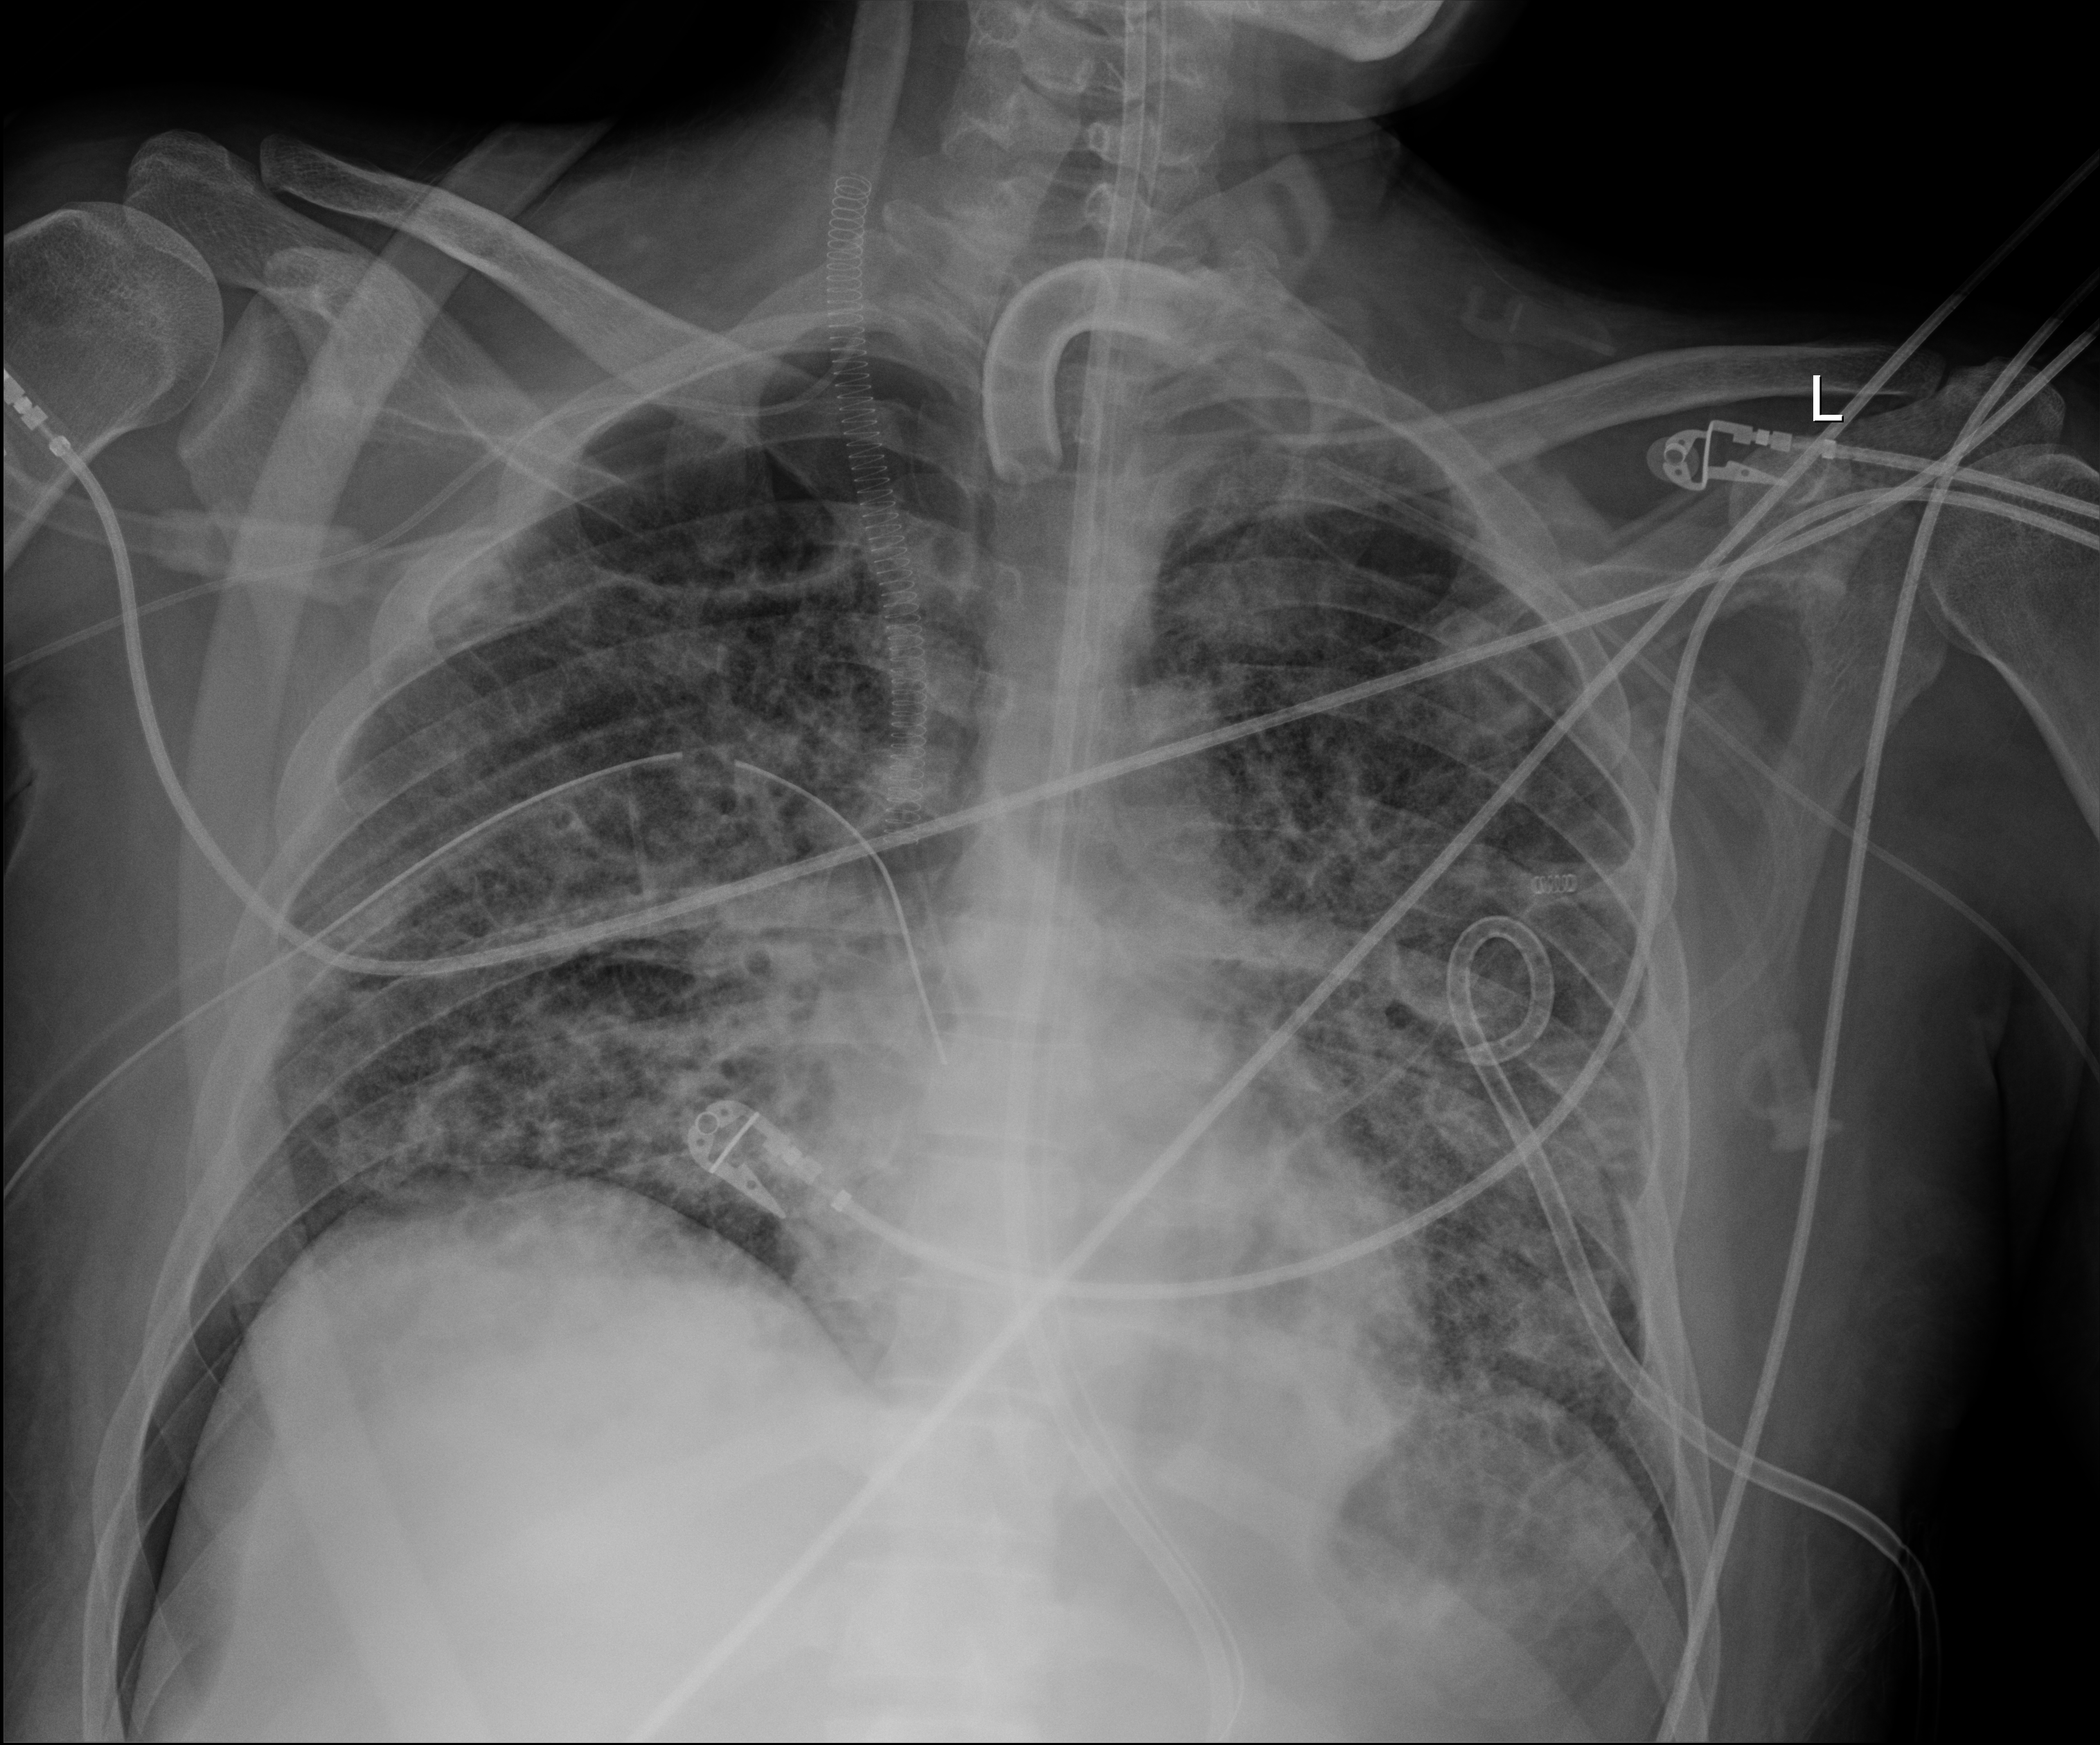
Chest X-ray. Patient hospitalised with COVID-19, aged 18–59 years.
Admission-level facts for this patient (not findings on this image; timing relative to this image not recorded): length of hospital stay: 60 days; mechanically ventilated during this hospital stay: yes.